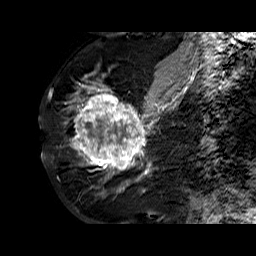
Breast MRI (dynamic contrast-enhanced), one sagittal slice. Position 29 of 60 along the scan axis. Dynamic contrast-enhanced series, time point 2 of 6 at this slice position (early post-contrast). 1.5 T. TE 6.3 ms, TR 32.4 ms. 4 mm slice thickness. 256 × 256 image matrix, field of view 200 × 200 mm. Female patient. From the clinical record (not read from this slice): setting: breast cancer imaged before/during neoadjuvant chemotherapy; receptor status: HR-positive, HER2-negative.
Outlined on this slice (semi-automatic segmentation, software-assisted and operator-edited):
- analysis volume of interest (the breast-tissue region the enhancement analysis was run in; not a lesion): bounding box [x1, y1, x2, y2] px = [68, 72, 177, 181]
- tumour enhancement mask (voxels above the 100 % enhancement threshold inside the analysis volume of interest): [69, 83, 174, 181]